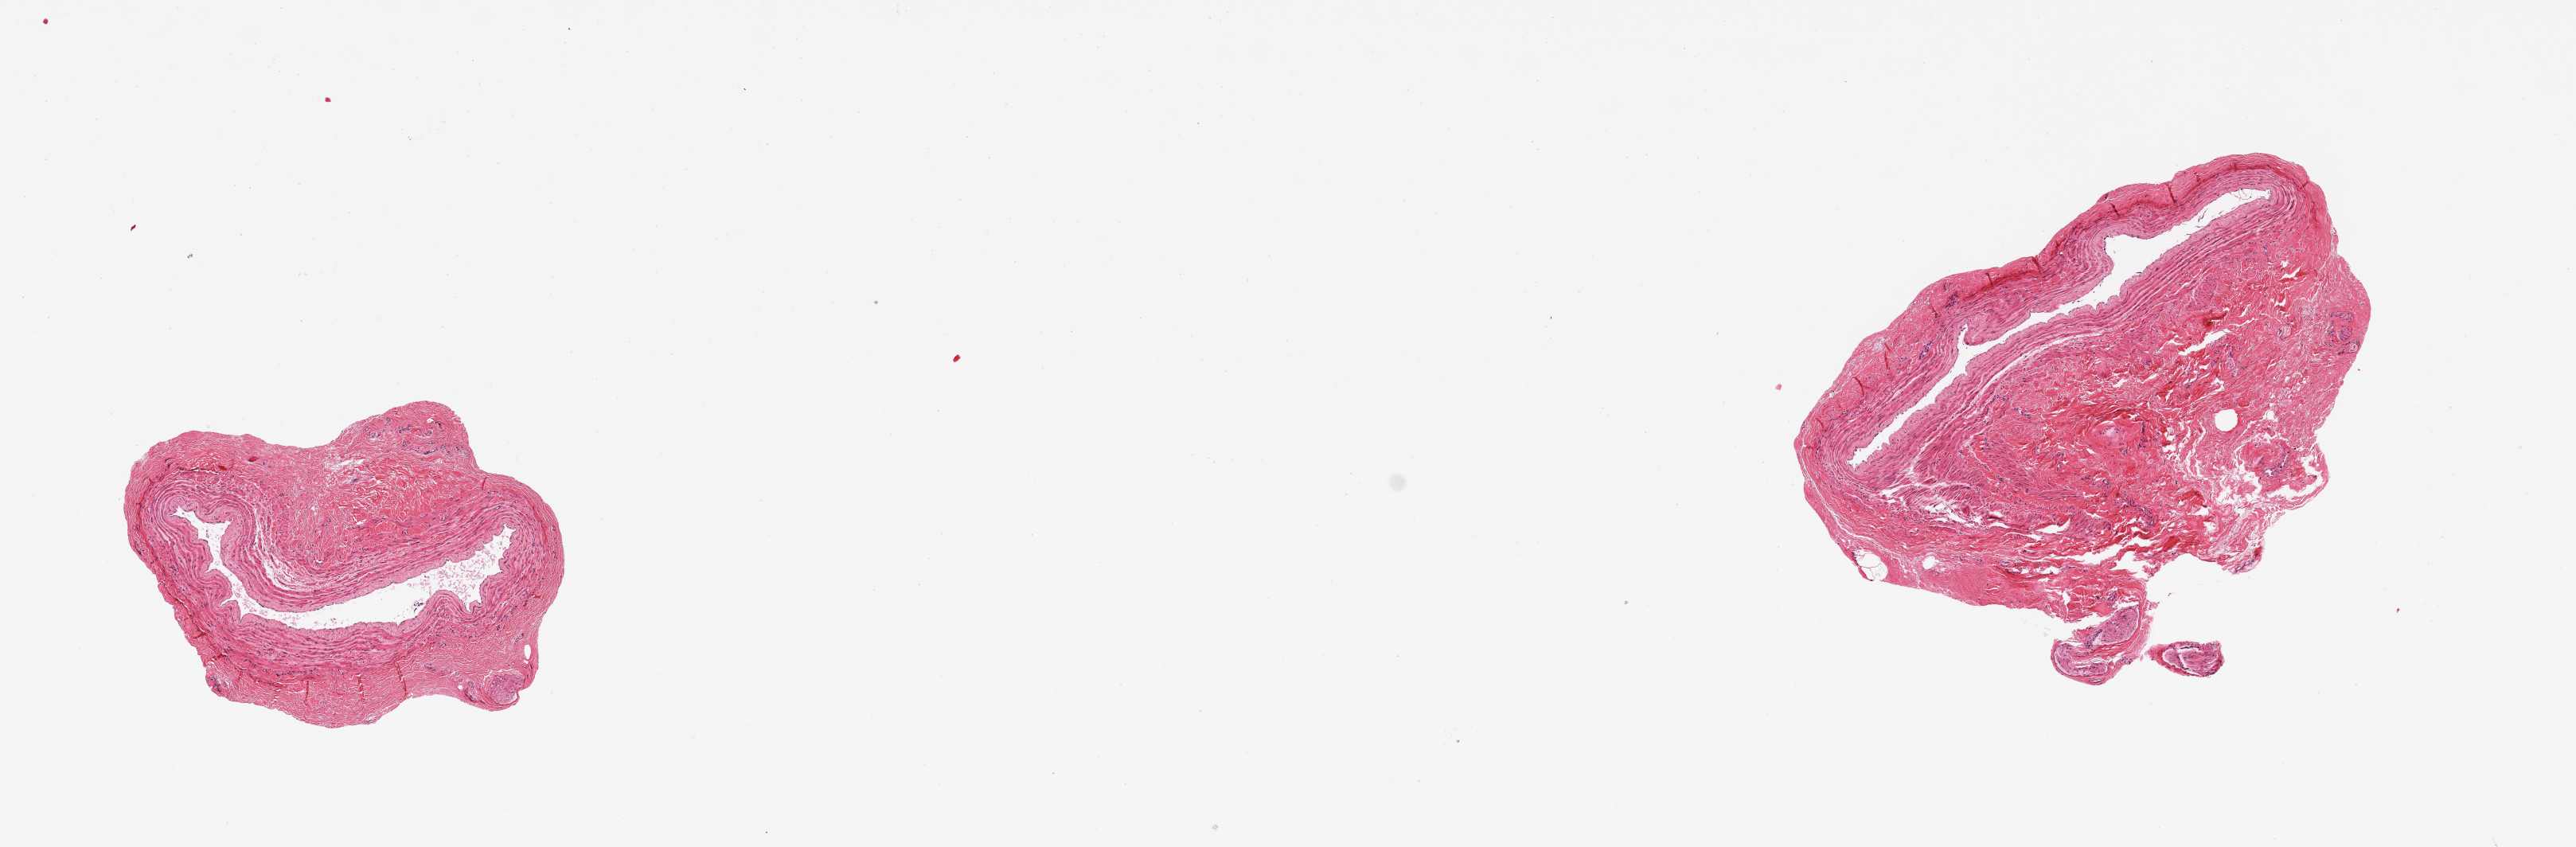
Haematoxylin and eosin whole-slide image, shown as a low-resolution overview of the whole scanned area (about 12.8 x 4.2 mm); PAXgene-fixed paraffin-embedded (PFPE) section; section of tibial artery (target tissue); donor tissue sample. Donor: female.
Reviewer comment on this tissue sample: 2 pieces: 1 with 60% perivascular stroma, other with 20%.